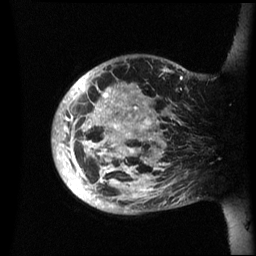
Breast MRI (dynamic contrast-enhanced), one sagittal slice. Slice 11 of 60 in the series (ordered by position). Dynamic contrast-enhanced series, image 2 of 3 at this slice position (ordered by acquisition). 1.5 T. TE 4.2 ms, TR 8.4 ms. 2.4 mm slice thickness. 256 × 256 image matrix, field of view 230 × 230 mm. Patient: female, 48 years.
Annotated regions visible in this slice (semi-automatic segmentation, software-assisted and operator-edited):
- analysis volume of interest (the breast-tissue region the enhancement analysis was run in; not a lesion): bounding box <52,55,202,214> (left, top, right, bottom; pixels)
- tumour enhancement mask (voxels above the 70 % enhancement threshold inside the analysis volume of interest): <52,69,182,198>